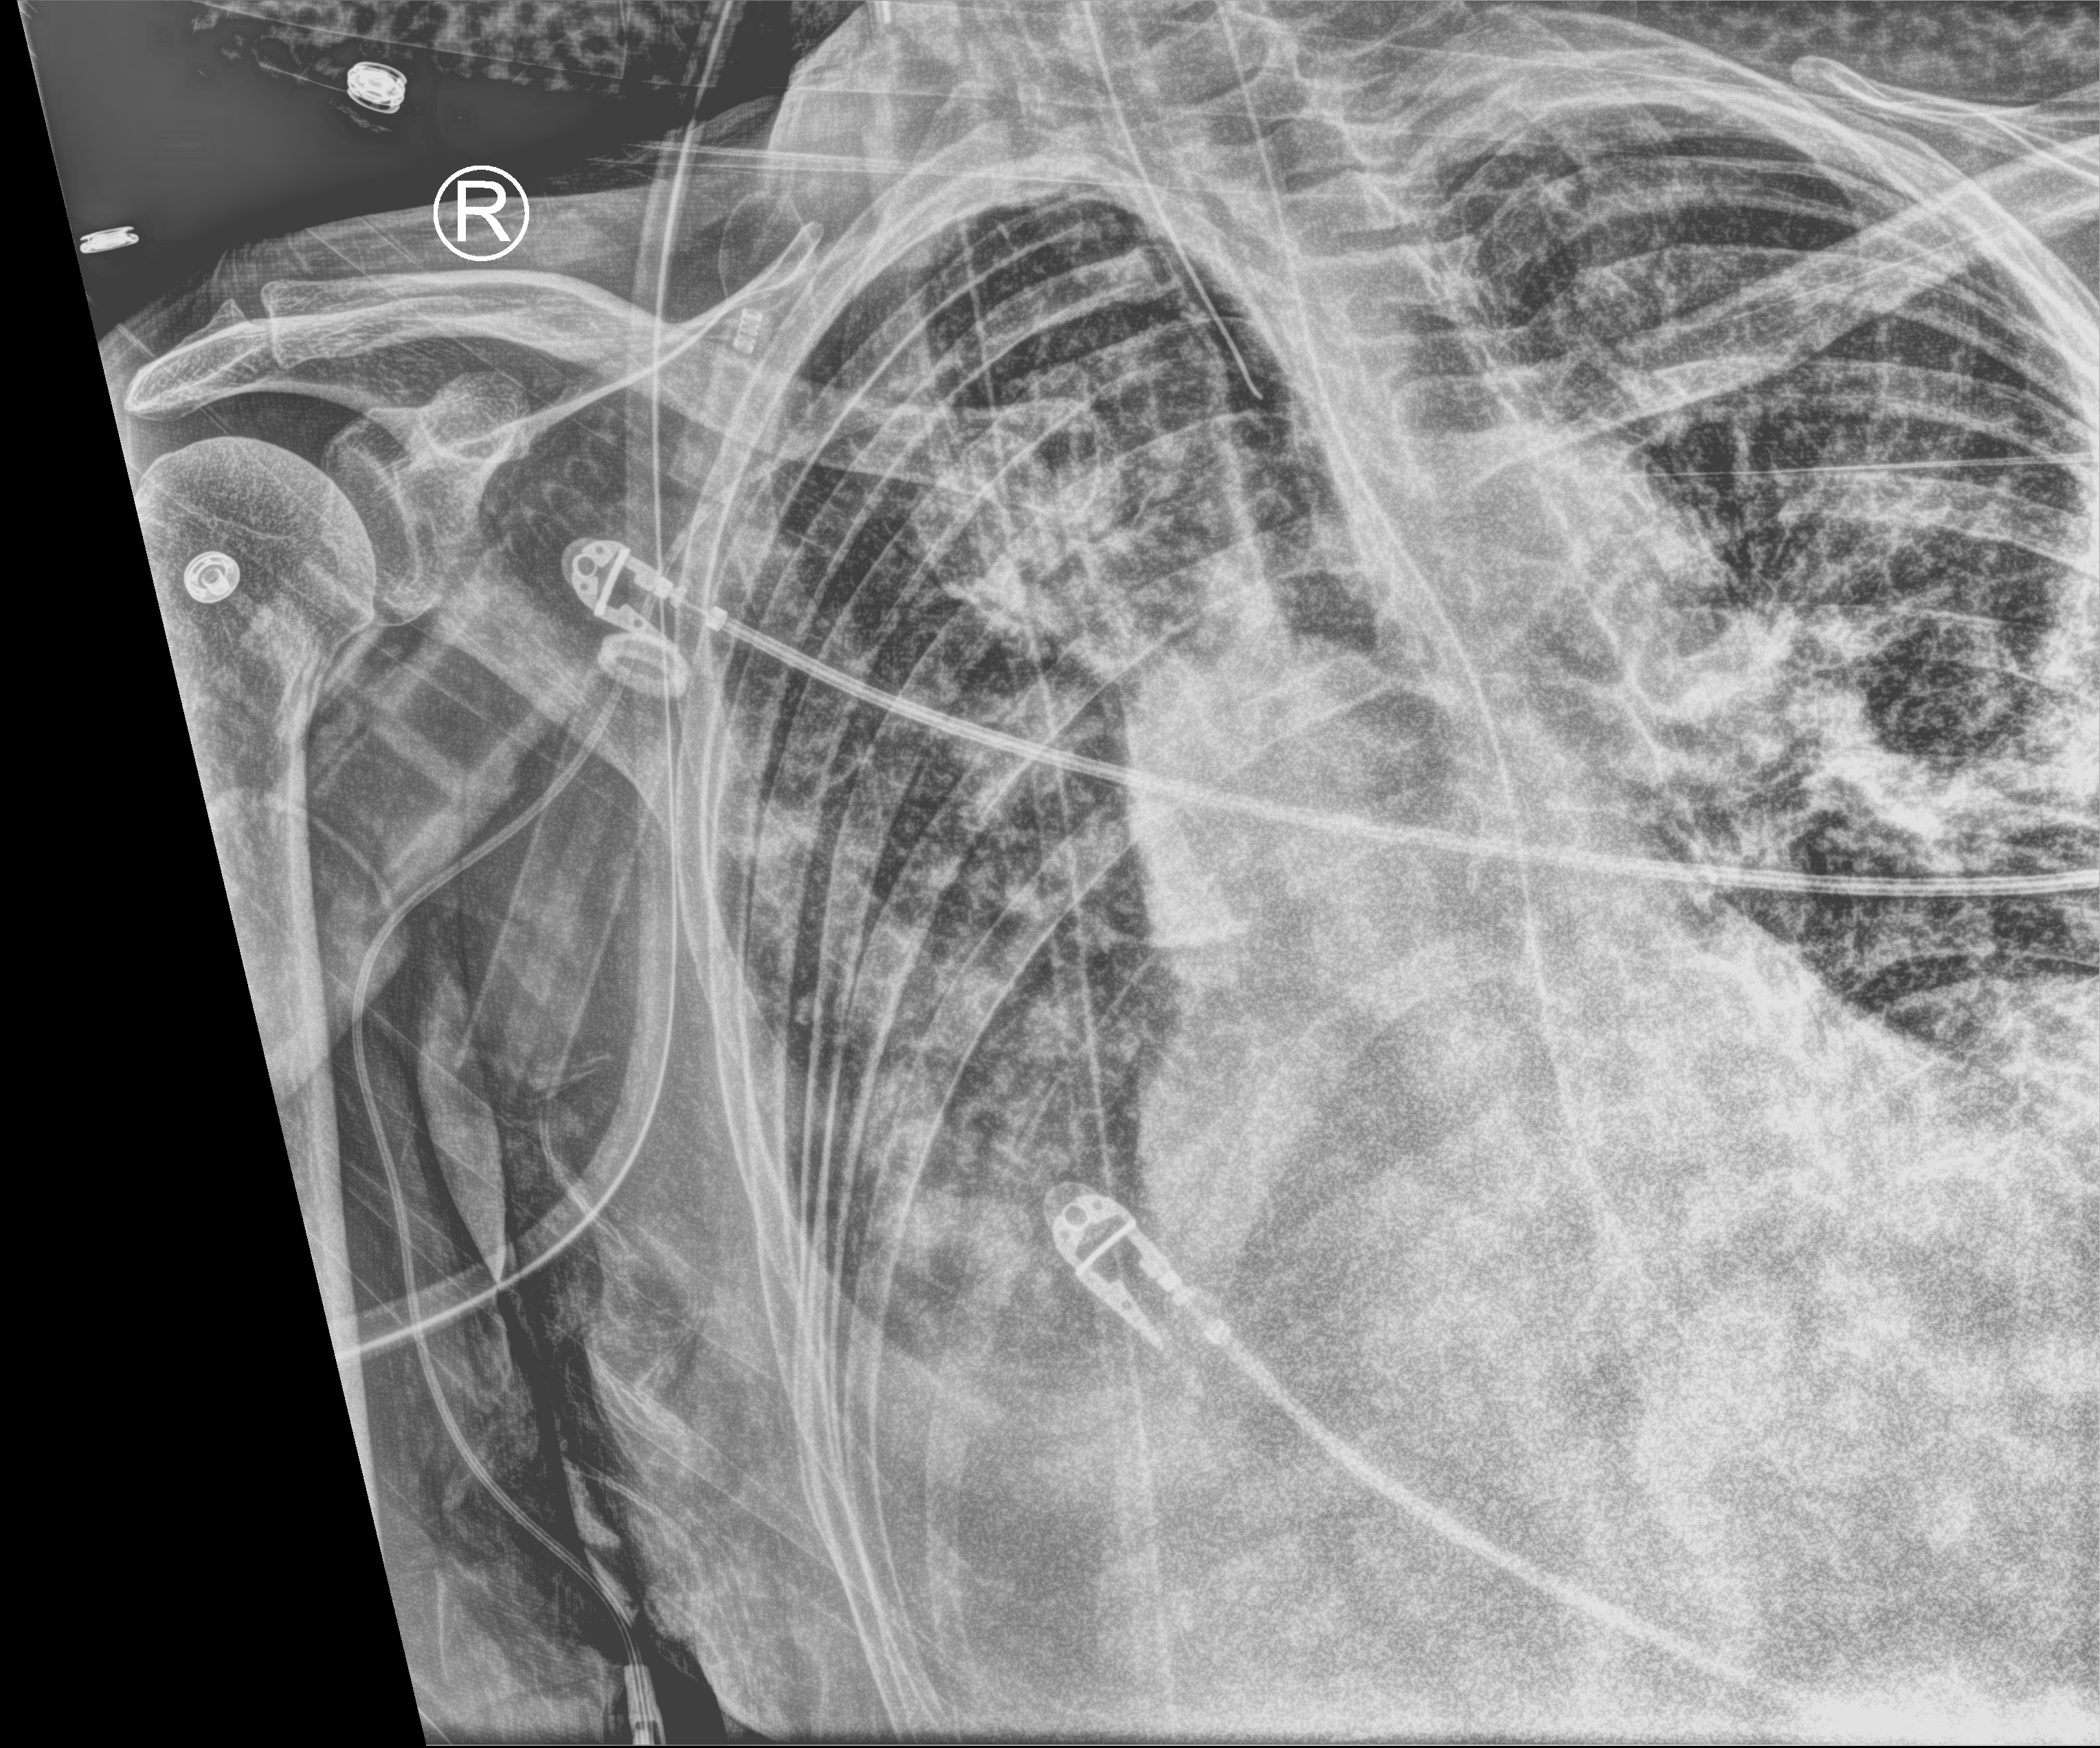
Portable chest radiograph, anteroposterior (AP) projection. Male patient hospitalised with COVID-19, age 75–90 years.
From the hospital-stay record, not from the radiograph (when in the stay this image was taken is not recorded): length of hospital stay: 70 days; mechanically ventilated during this hospital stay: yes.